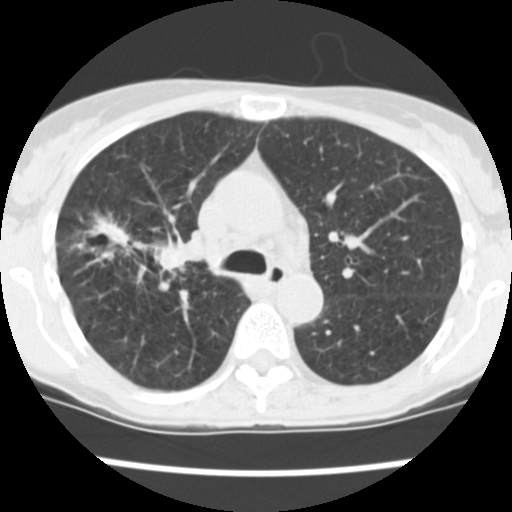
Low-dose screening chest CT, one axial slice. Slice 164 of 252 in the series (ordered by position). Lung window (W 1500 / L -600 HU). 2.5 mm slice thickness. 512 × 512 image matrix, field of view 276 × 276 mm.
Outlined on this slice (manually delineated by an expert):
- lesion 2 (tumor, lower lobe of right lung): bounding box [x1, y1, x2, y2] px = [87, 214, 204, 275]